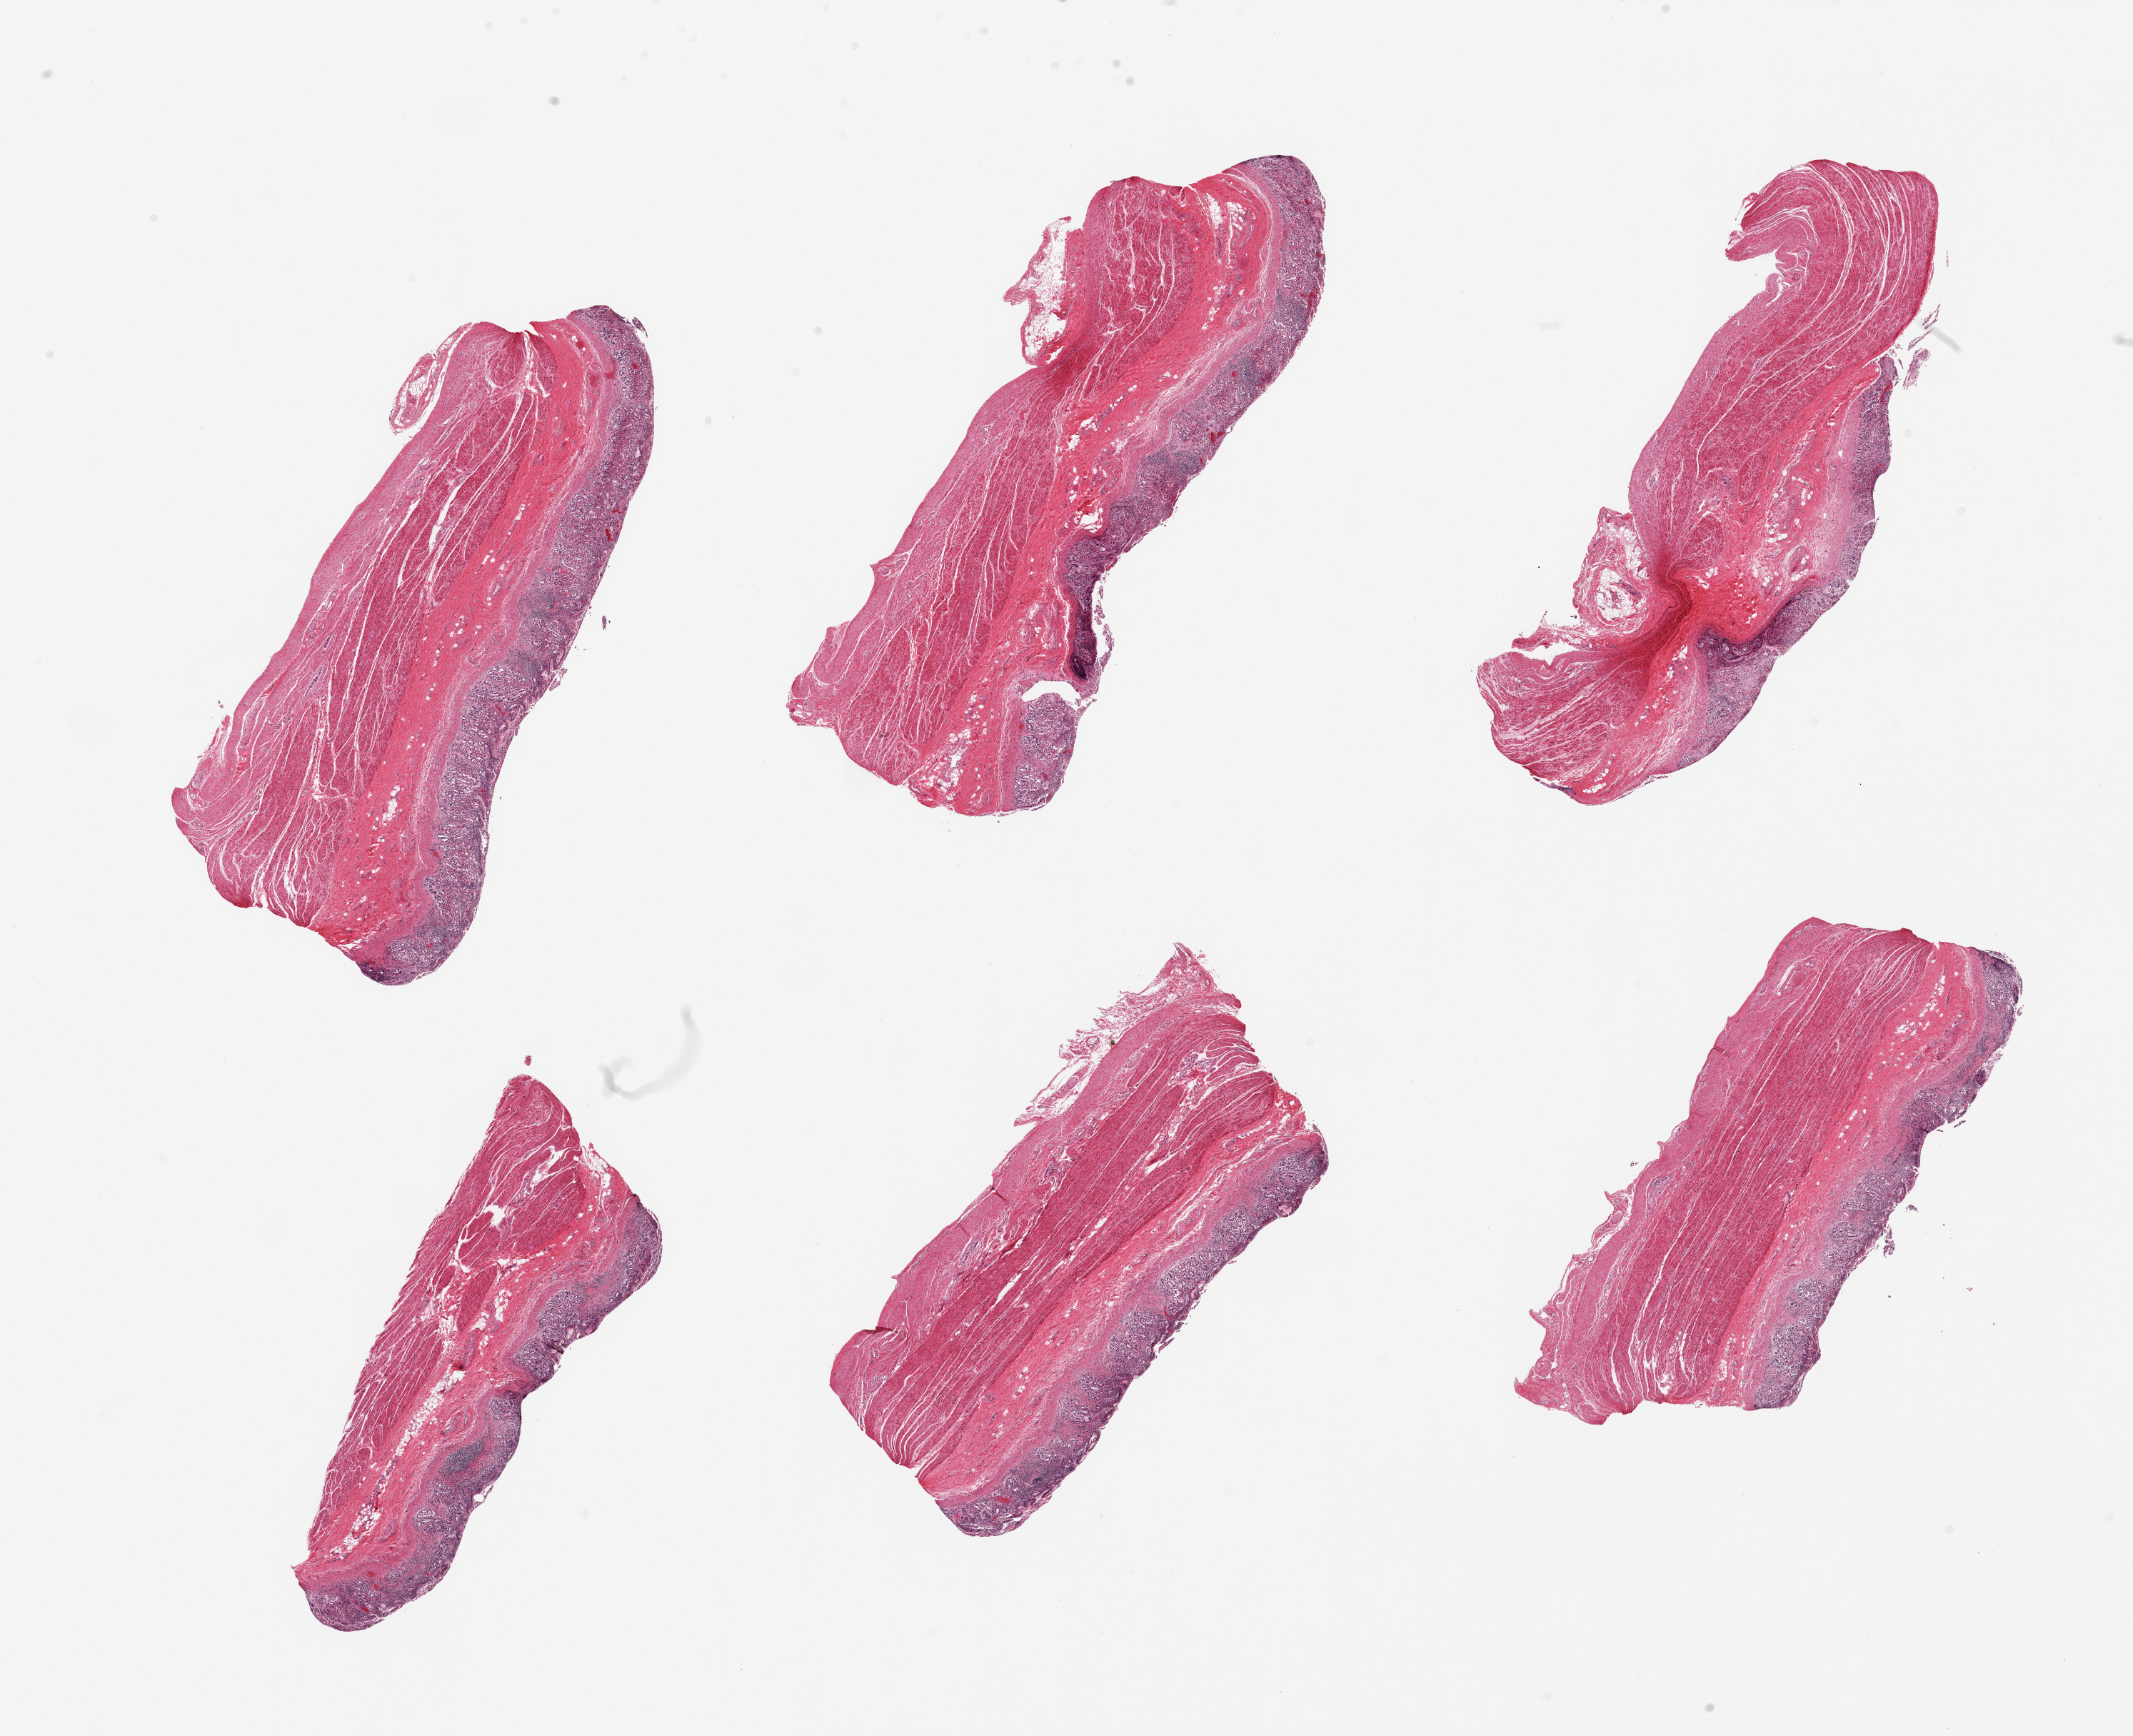
Whole-slide image, haematoxylin and eosin stain — a low-resolution overview of the entire scanned area, about 23.6 x 19.2 mm (slide scanned at 20x), PAXgene-fixed, paraffin-embedded tissue, sampled site (target tissue): stomach, tissue donor sample.
Reviewer comment on this tissue sample: 6 pieces, diffuse chronic gastritis; prominent ganglion cells in muscularis propria.